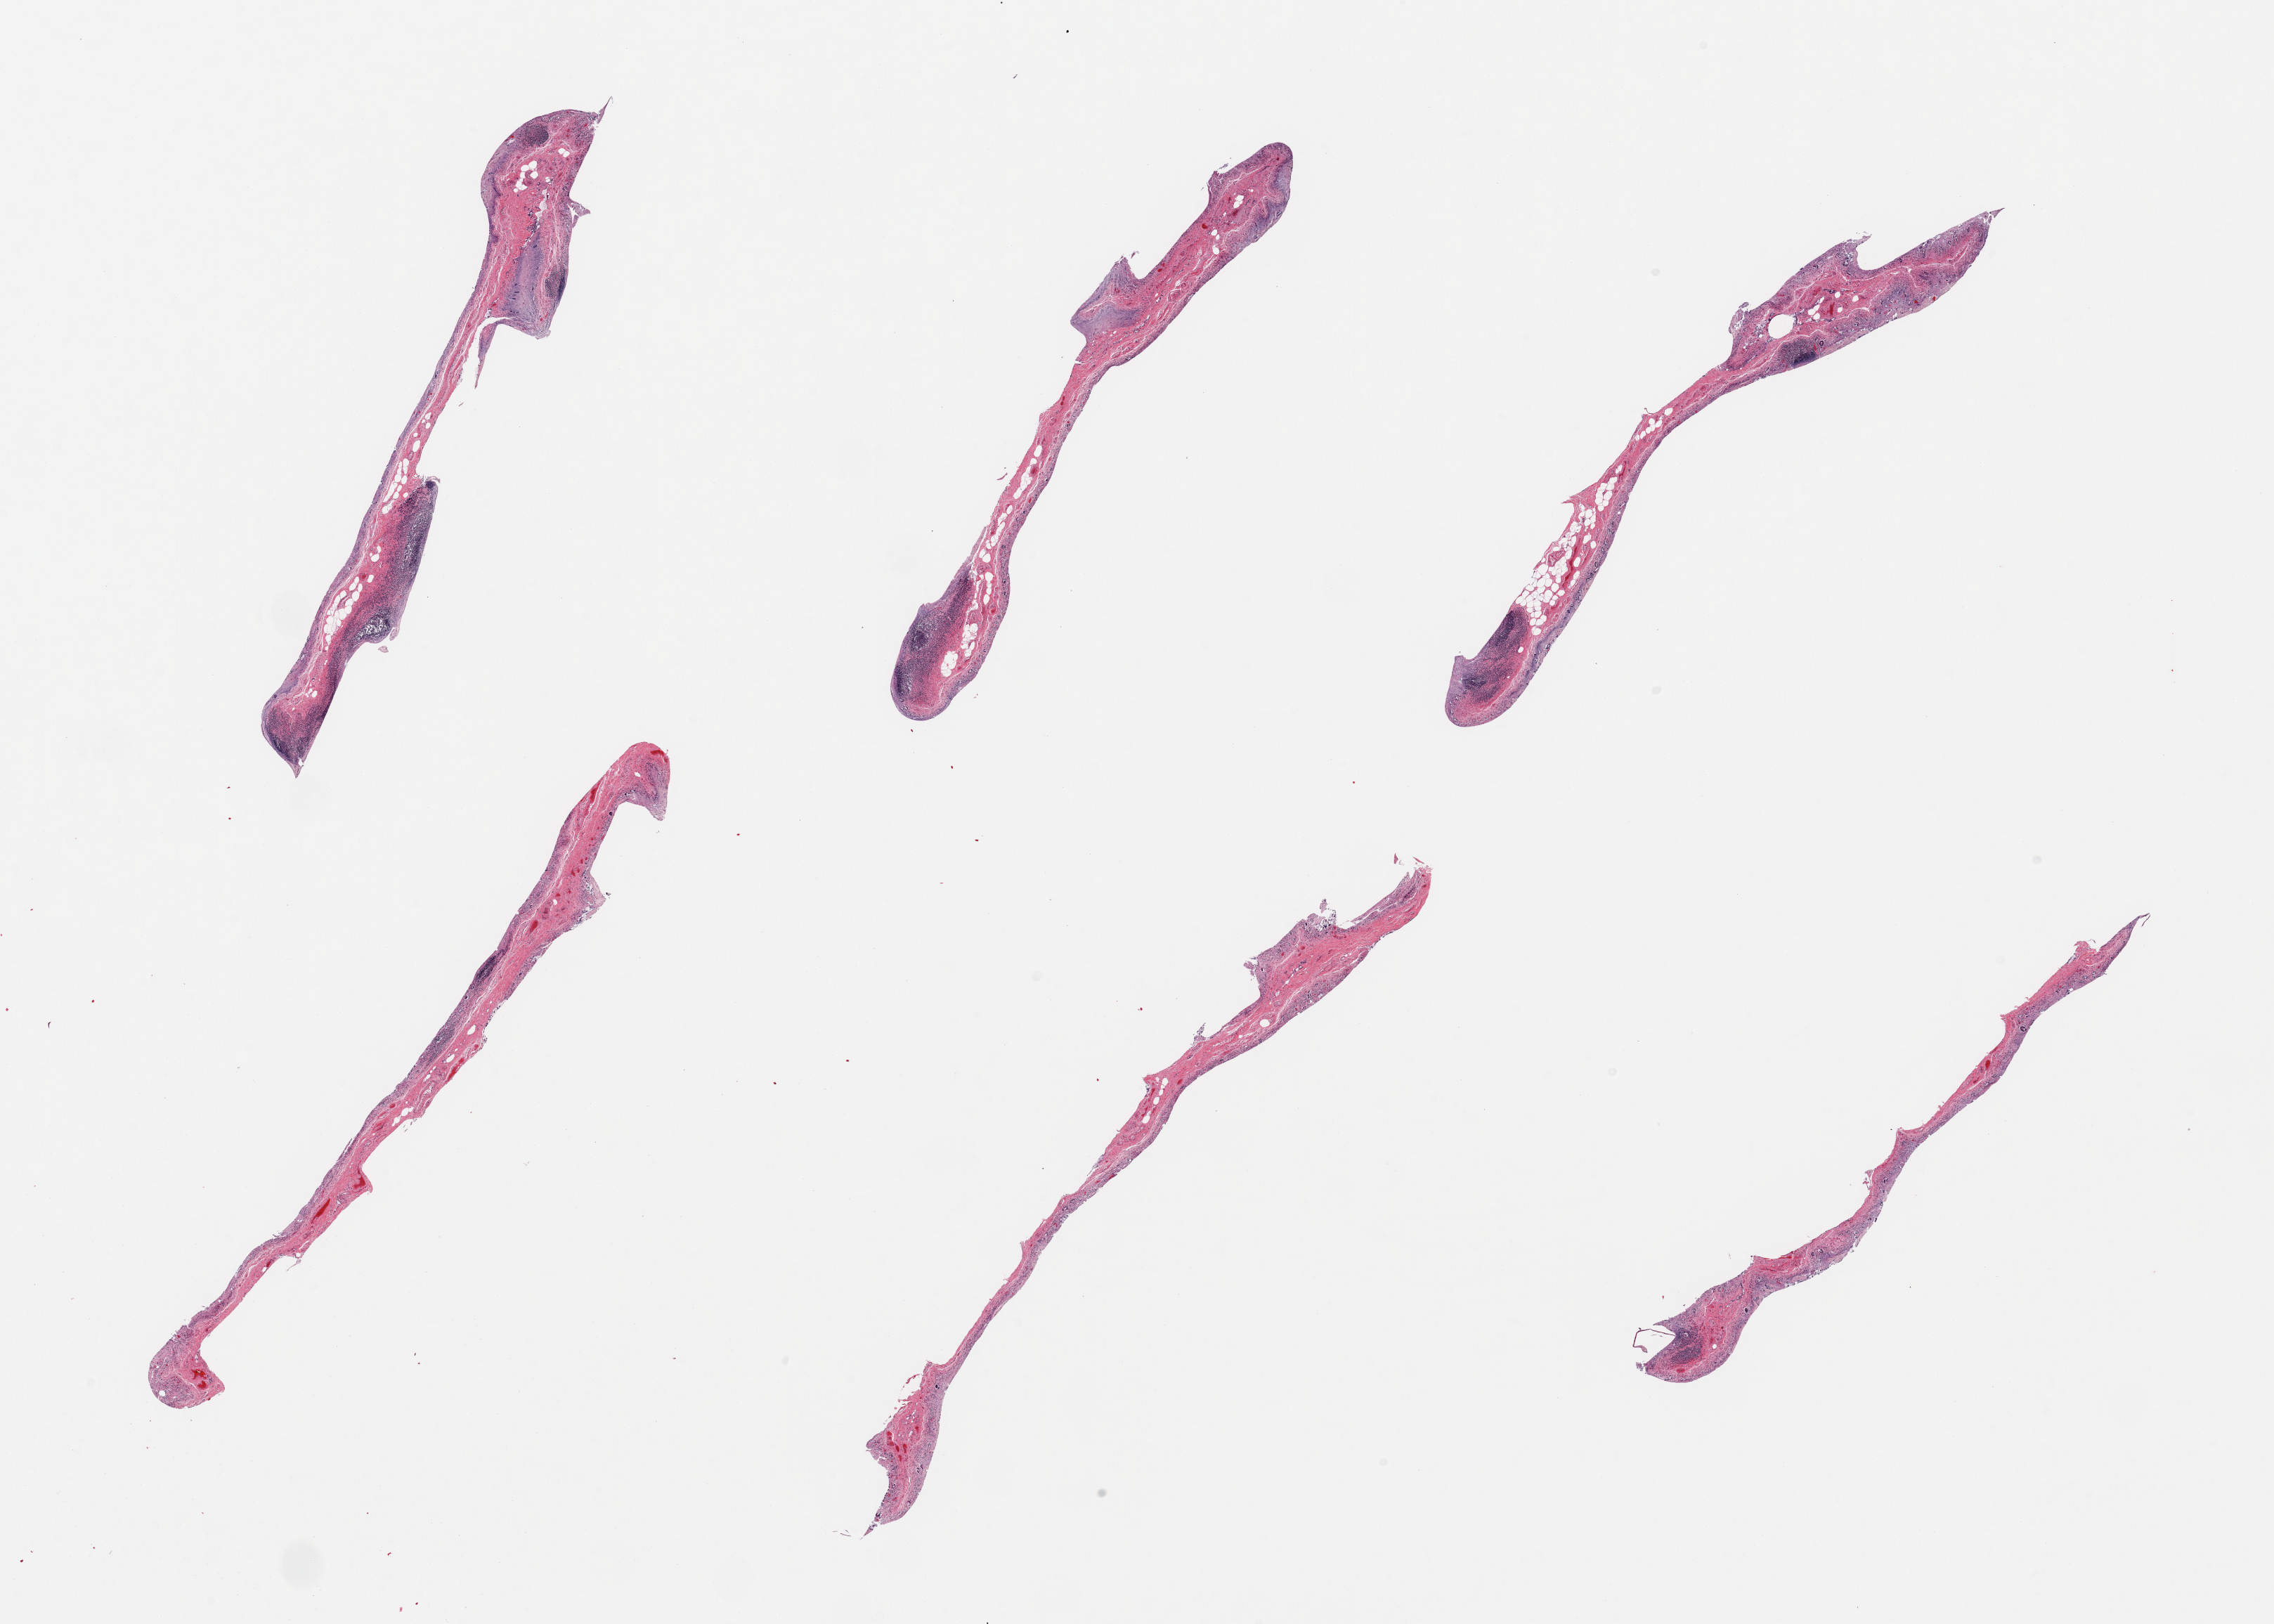
Whole-slide image, haematoxylin and eosin stain — low-resolution overview of the scanned area, about 25.6 x 18.3 mm (slide scanned at 20x), PAXgene-fixed, paraffin-embedded tissue, sampled site (target tissue): ileum, donor tissue sample. Donor sex: male.
Pathologist's review note for this sample: 6 pieces, glandular mucosa with advanced autolysis; target lymphoid aggregates are ~20% residual tissue.